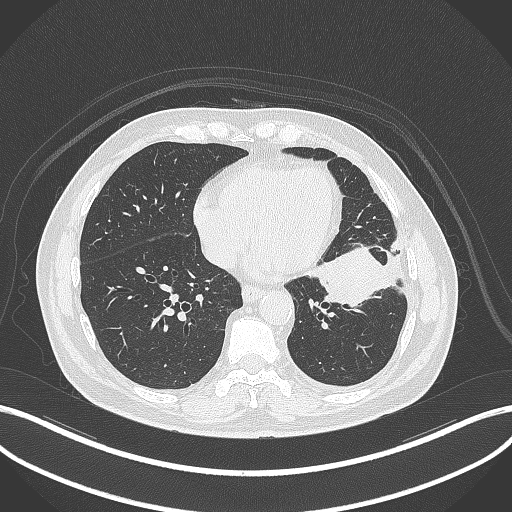
Chest CT, one axial slice; slice 128 of 230 in the series (ordered by position); reconstruction kernel B70f; lung window (W 1500 / L -600 HU); 1 mm slice thickness; 512 × 512 image matrix, field of view 400 × 400 mm. Male patient, age 68 years. From the clinical record (not read from this slice): clinical TNM (as recorded): T2b N0 M0.
Annotated regions visible in this slice (bounding box drawn by a radiologist):
- lung tumour (recorded histology: squamous cell carcinoma): bounding box <307,246,401,312> (left, top, right, bottom; pixels)